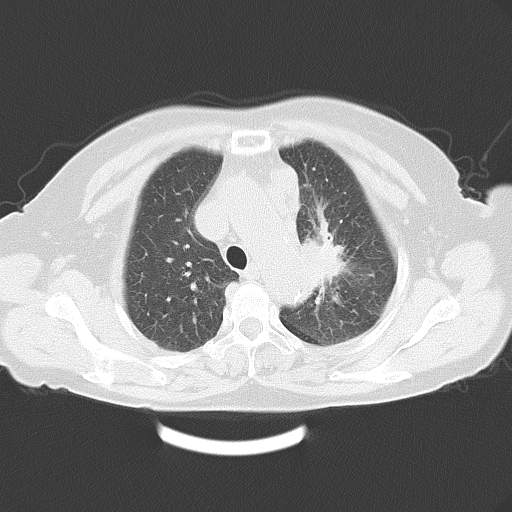
Chest CT, one axial slice; reconstruction kernel B70f; 120 kVp; lung window (W 1500 / L -600 HU); 512 × 512 image matrix. Female patient, age 71 years. Case-level facts recorded for this patient, not image findings: clinical TNM (as recorded): T3 N3 M0.
Annotated regions visible in this slice (rectangle marked by the reading radiologist):
- lung tumour (recorded histology: adenocarcinoma): box from (x=299, y=236) to (x=370, y=292) px